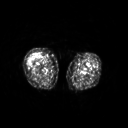
FDG PET of an extremity soft-tissue mass (from a PET/CT study), one axial slice. Slice 210 of 311 in the series (ordered by position). 3.27 mm slice thickness. 128 × 128 image matrix, field of view 500 × 500 mm. Female patient, age 57 years. From the clinical record (not read from this slice): histological type: pleiomorphic undifferentiated sarcoma; grade: high; site of the primary tumour: right quadricep.
Outlined on this slice (expert contour drawn on MRI and transferred to this co-registered scan by the dataset authors):
- tumour plus oedema (research contour): bounding box (x1, y1, x2, y2) in pixels: (28, 52, 41, 66)